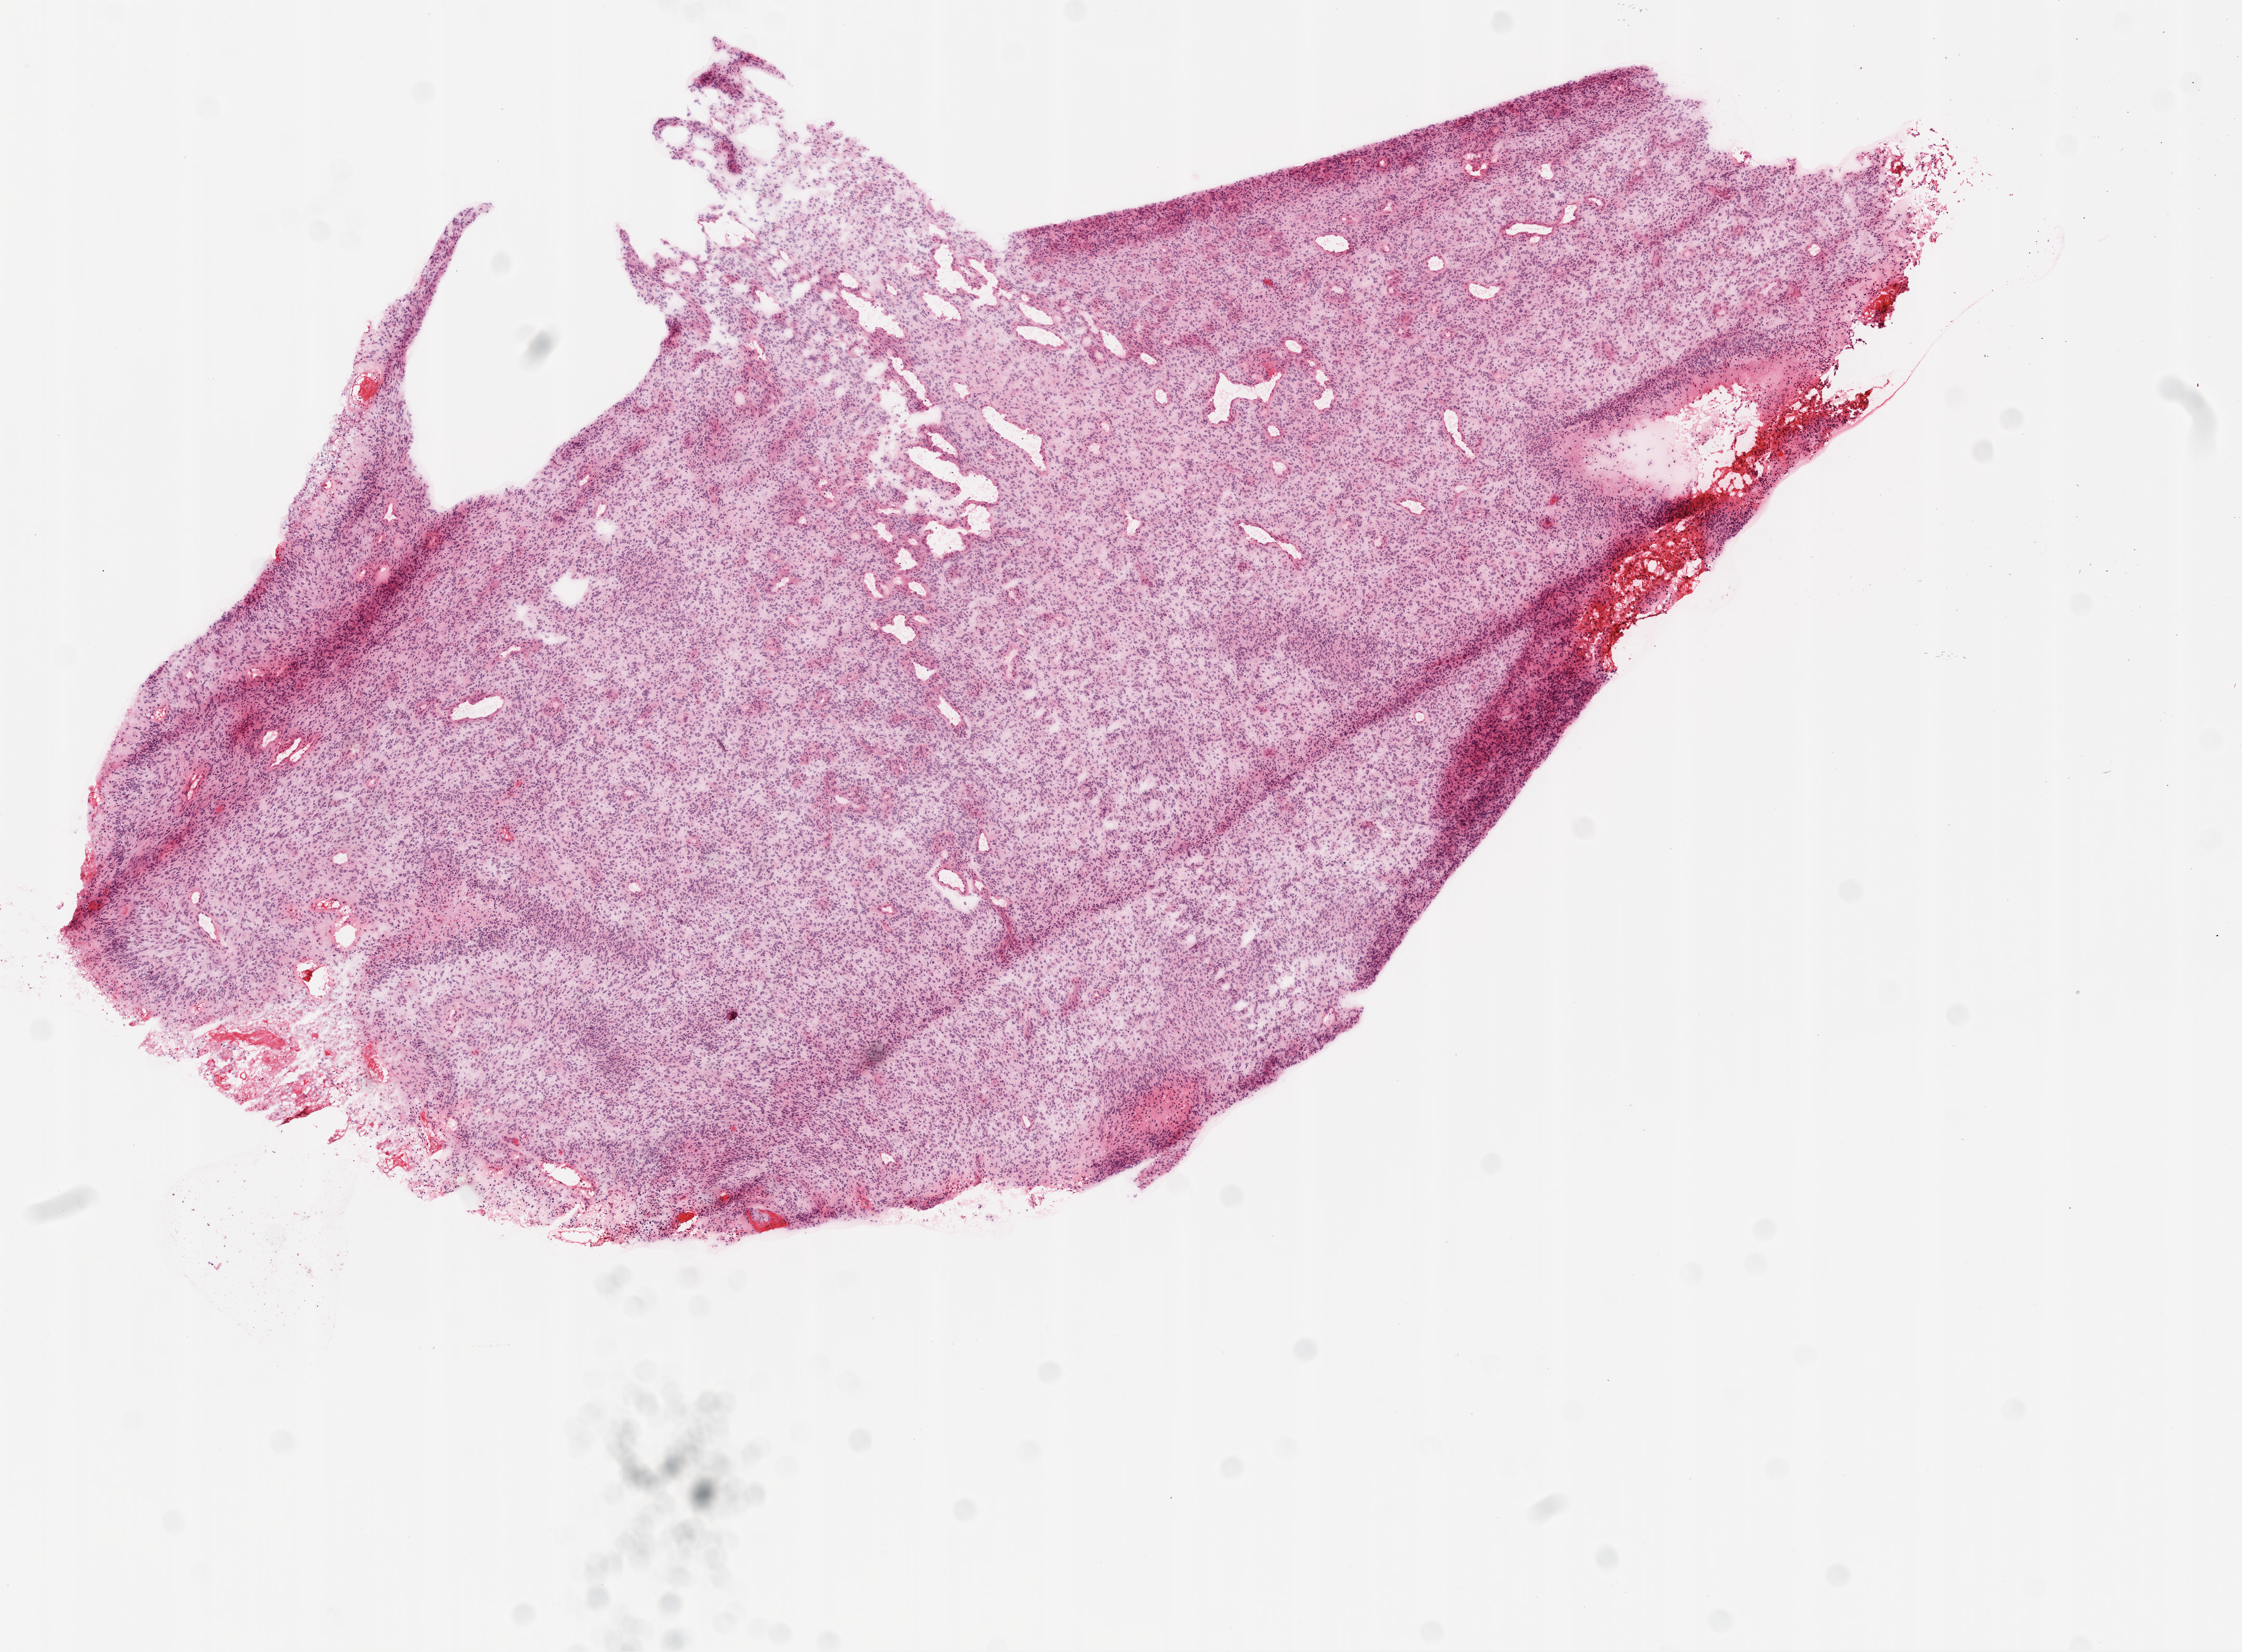
Whole-slide histology image, H&E, shown as a low-resolution overview of the whole scanned area (about 8.7 x 6.4 mm), frozen section, brain, primary tumour sample. Male patient; age at initial diagnosis 49 years. Slide review estimates, as recorded: tumour cells 95%, tumour nuclei 95%, normal cells 0%, stromal cells 0%, necrosis 5%.
• histologic diagnosis: Glioblastoma